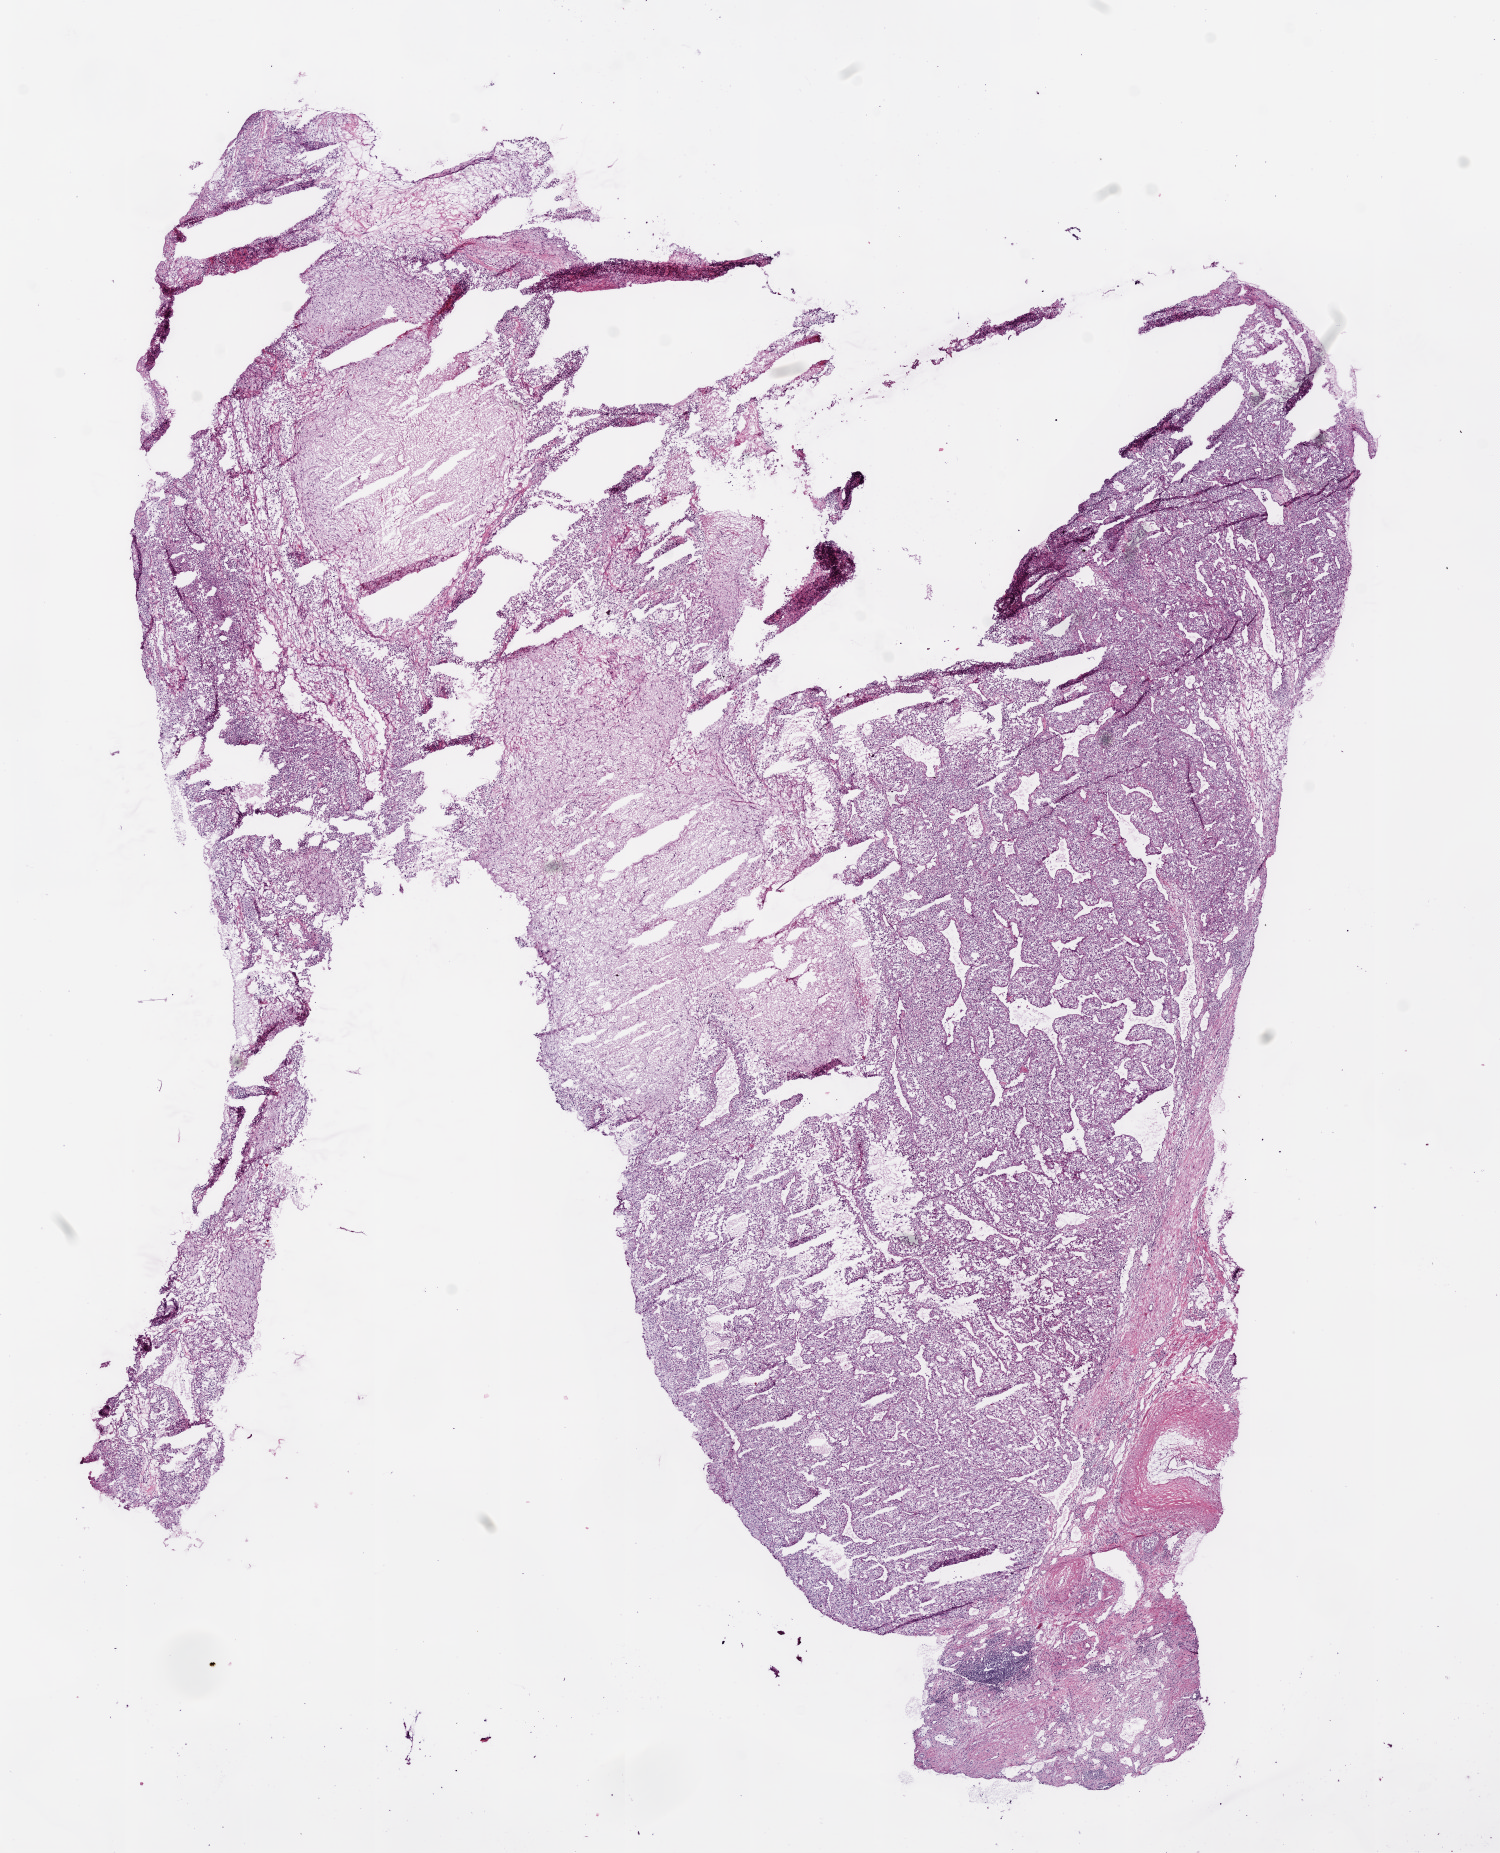
Whole-slide histology image, H&E, low-resolution overview of the scanned area, about 12.0 x 14.9 mm (from a 20x scan); frozen section from the bottom of the tissue portion; primary tumour sample from the kidney. Patient: male, age at initial diagnosis 79 years. Histologic grade: G3 (poorly differentiated). Pathologist review of this section (percent, as recorded): tumour cells 80%, tumour nuclei 75%, normal cells 0%, stromal cells 20%, necrosis 0%.
• lymph nodes positive (case pathology): 0 of 7 examined
• histologic diagnosis: Clear cell adenocarcinoma, NOS
• AJCC pathologic stage: II